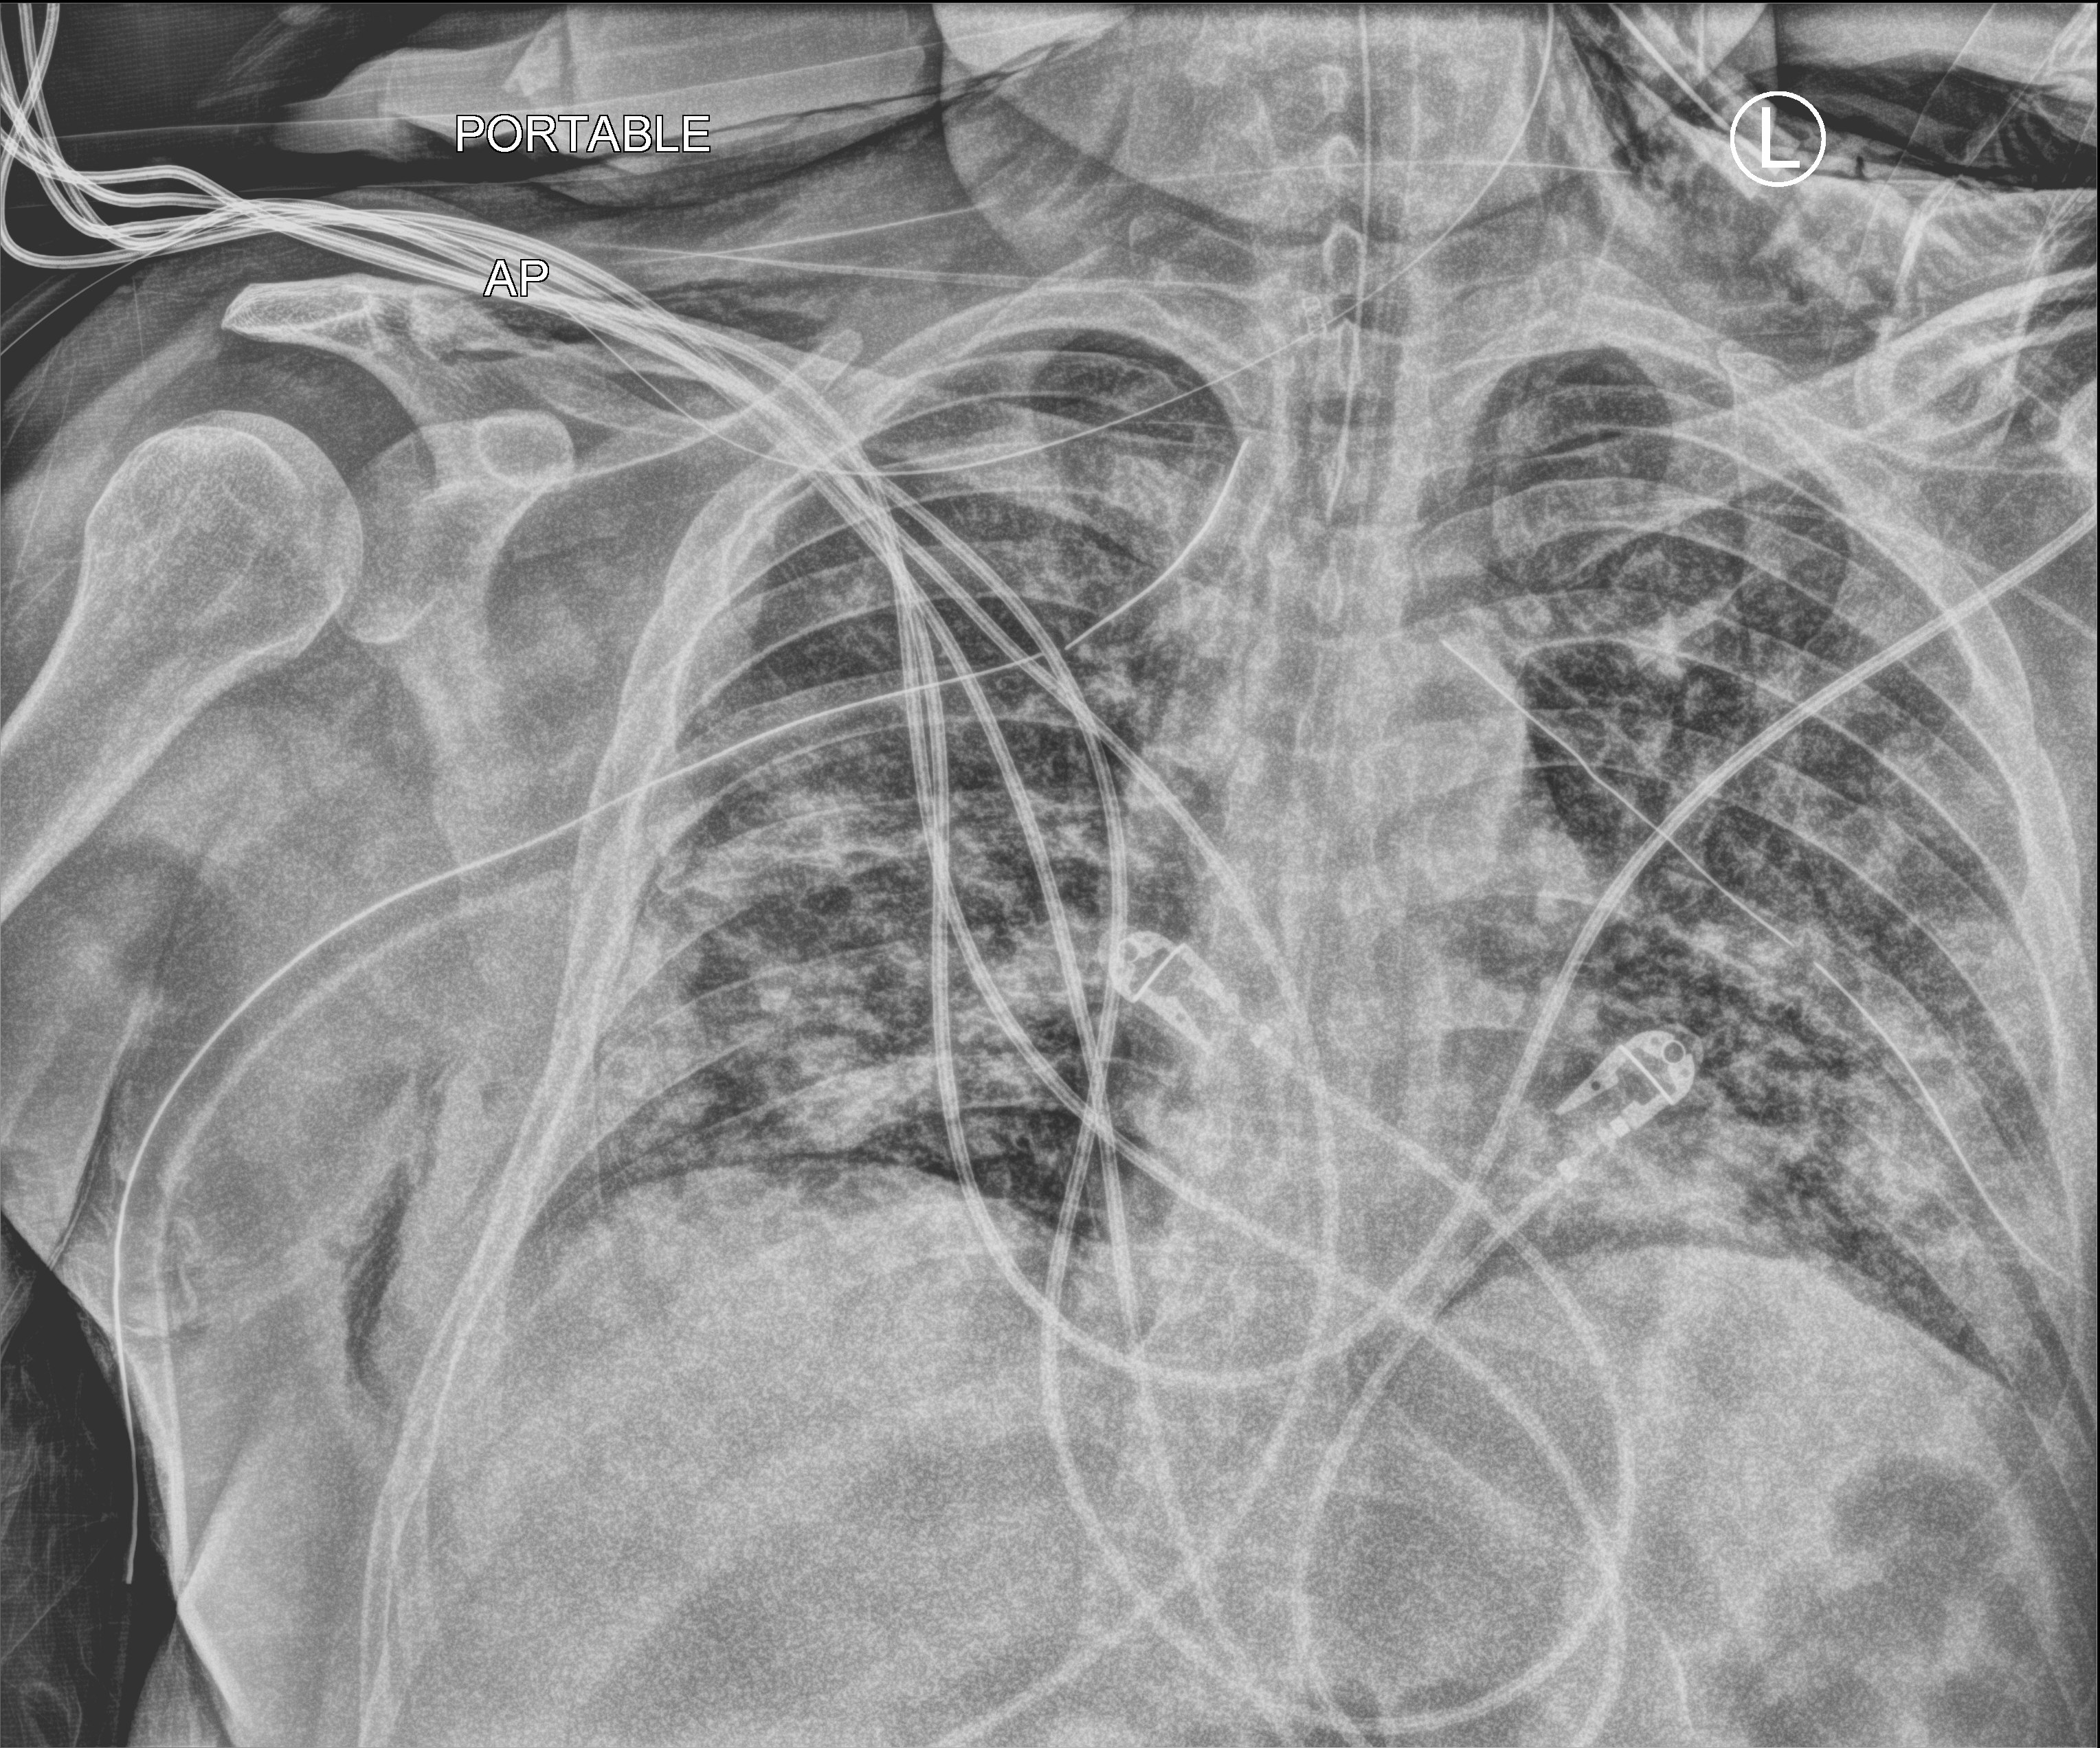
Chest X-ray (portable), anteroposterior (AP) projection. Male patient hospitalised with COVID-19, age 18–59 years.
Hospital-stay facts (about this admission, not read from this image; timing relative to this image not recorded): other chronic lung disease (admission record): no; admitted to intensive care during this hospital stay: yes.